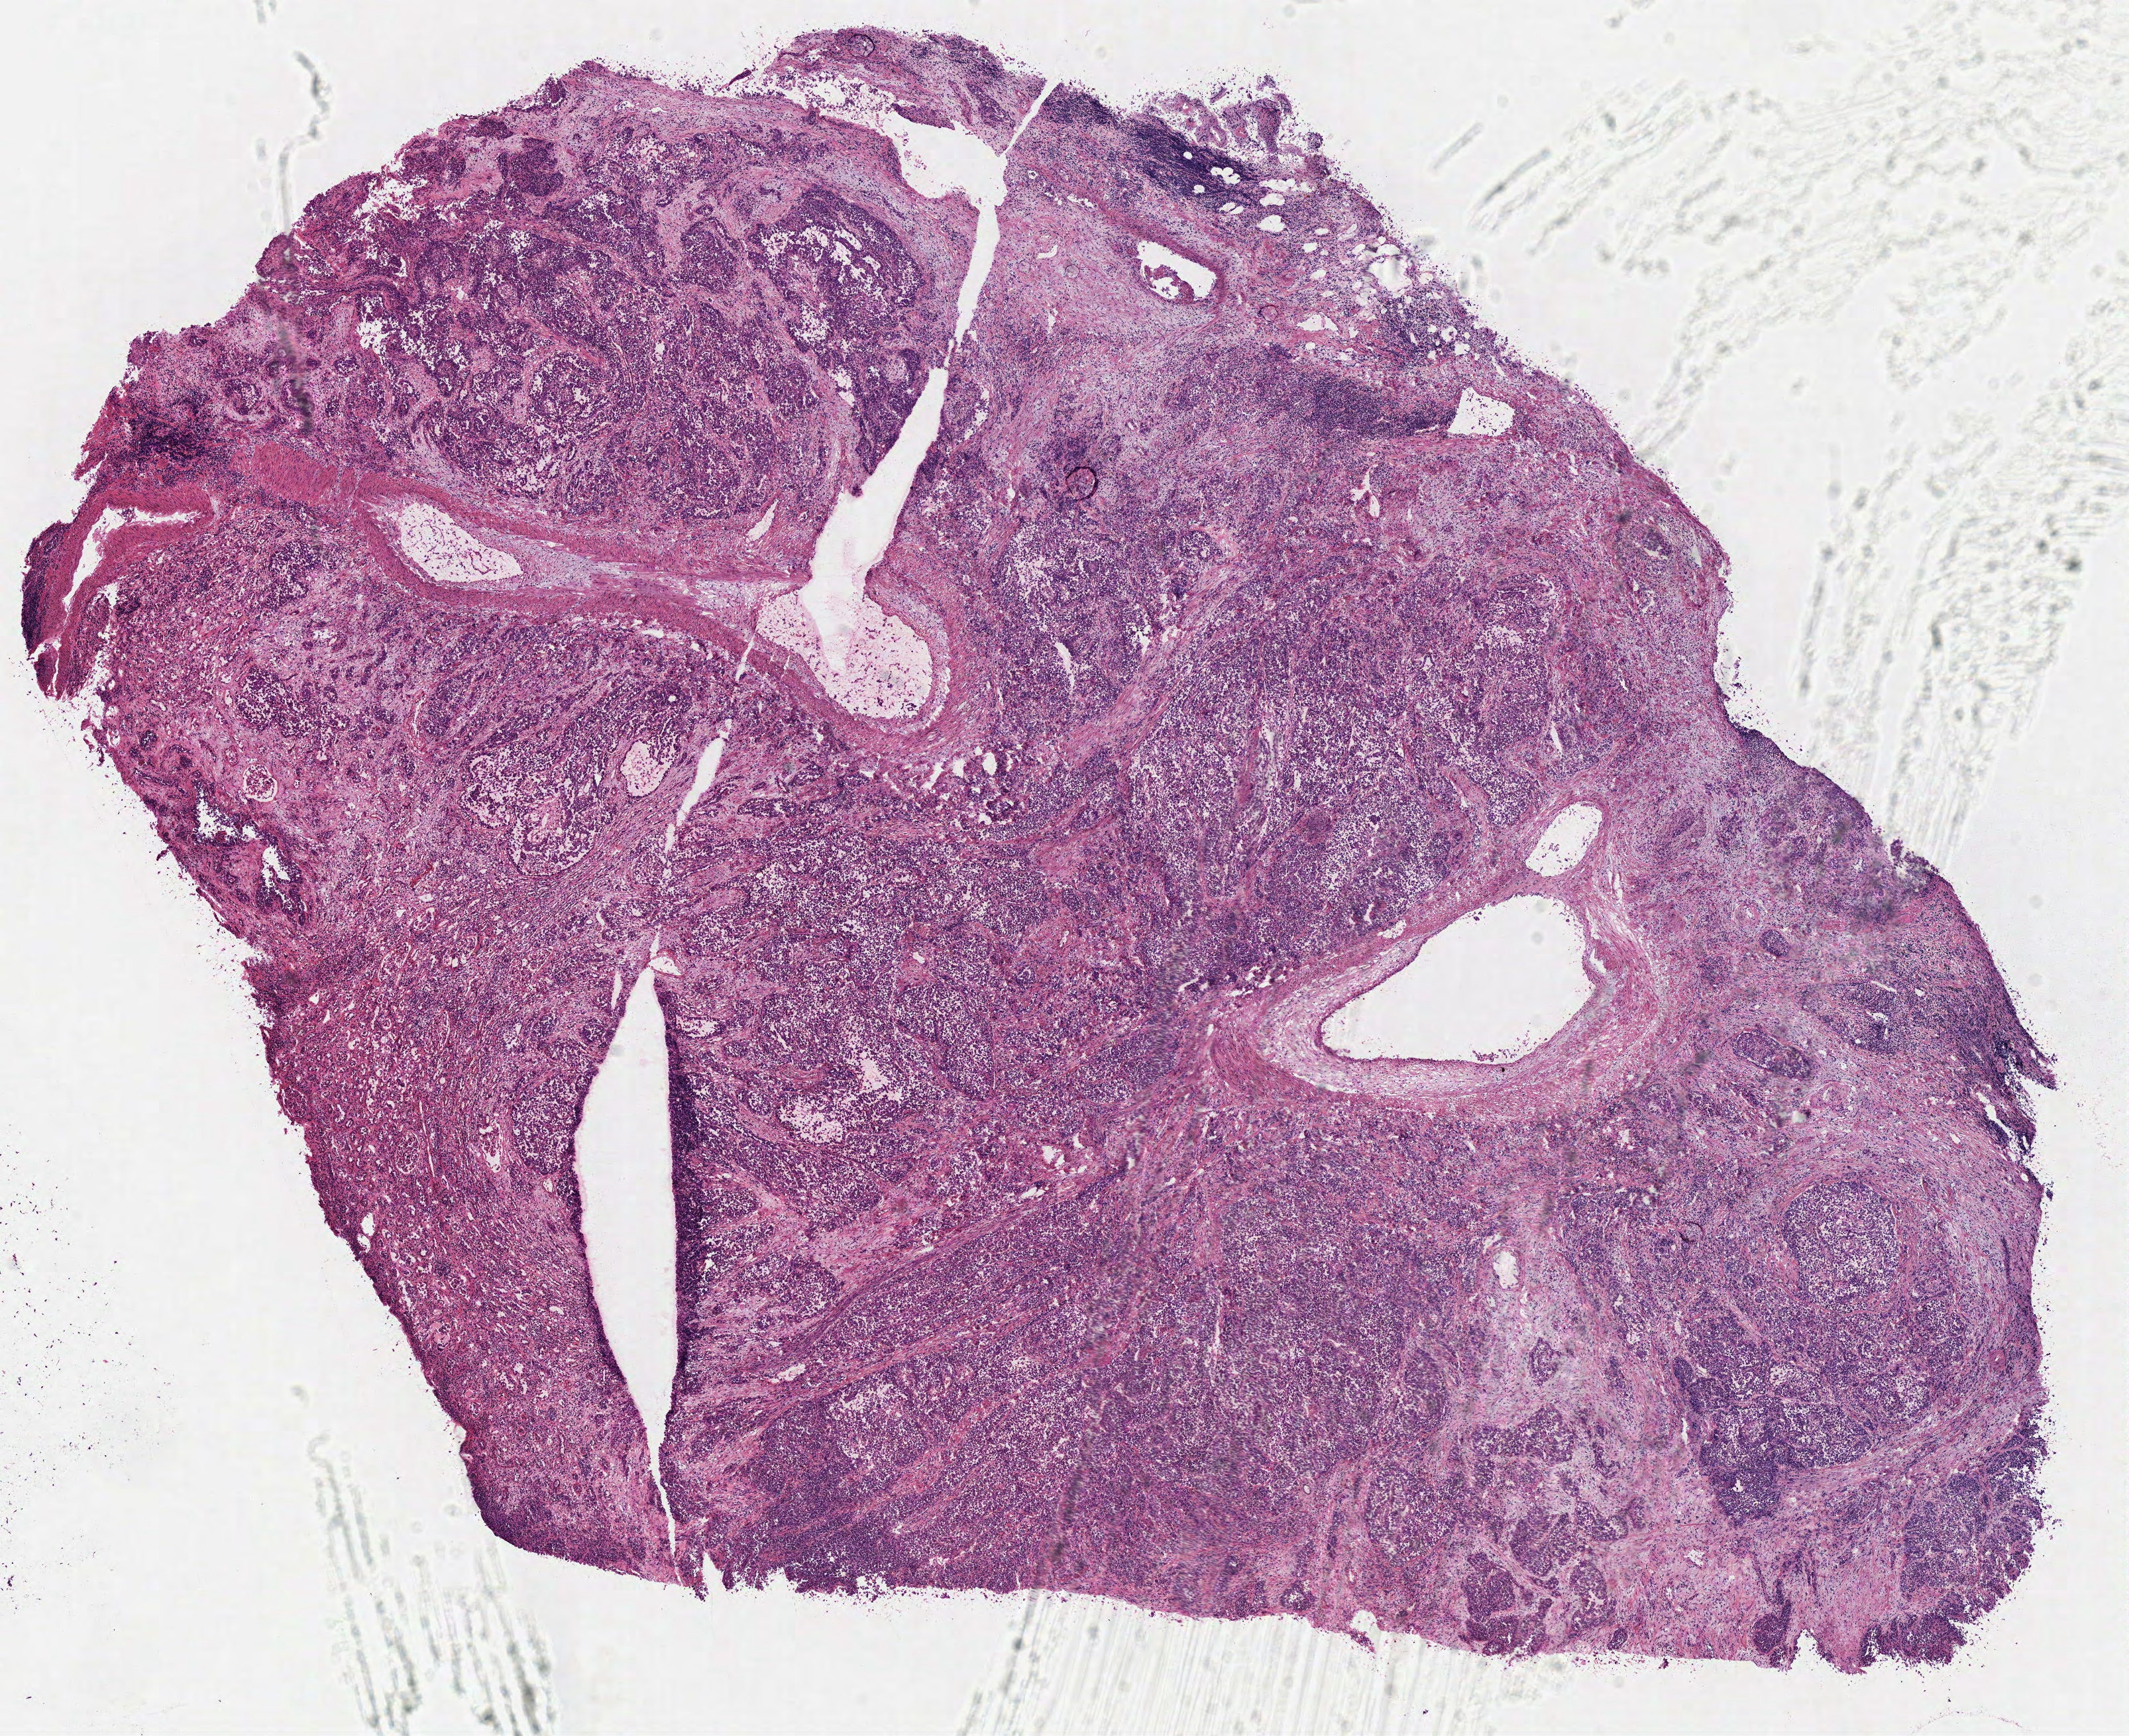
Hematoxylin and eosin (H&E) stained whole-slide image, whole scanned area (about 12.7 x 10.3 mm, slide scanned at 40x) shown as a low-resolution overview; frozen section; kidney, primary tumour sample. Patient: male, age at initial diagnosis 42 years. Slide review estimates, as recorded: tumour cells 85%, tumour nuclei 75%, normal cells 0%, stromal cells 15%, necrosis 0%.
Histologic diagnosis: Papillary adenocarcinoma, NOS. AJCC pathologic stage: IV.